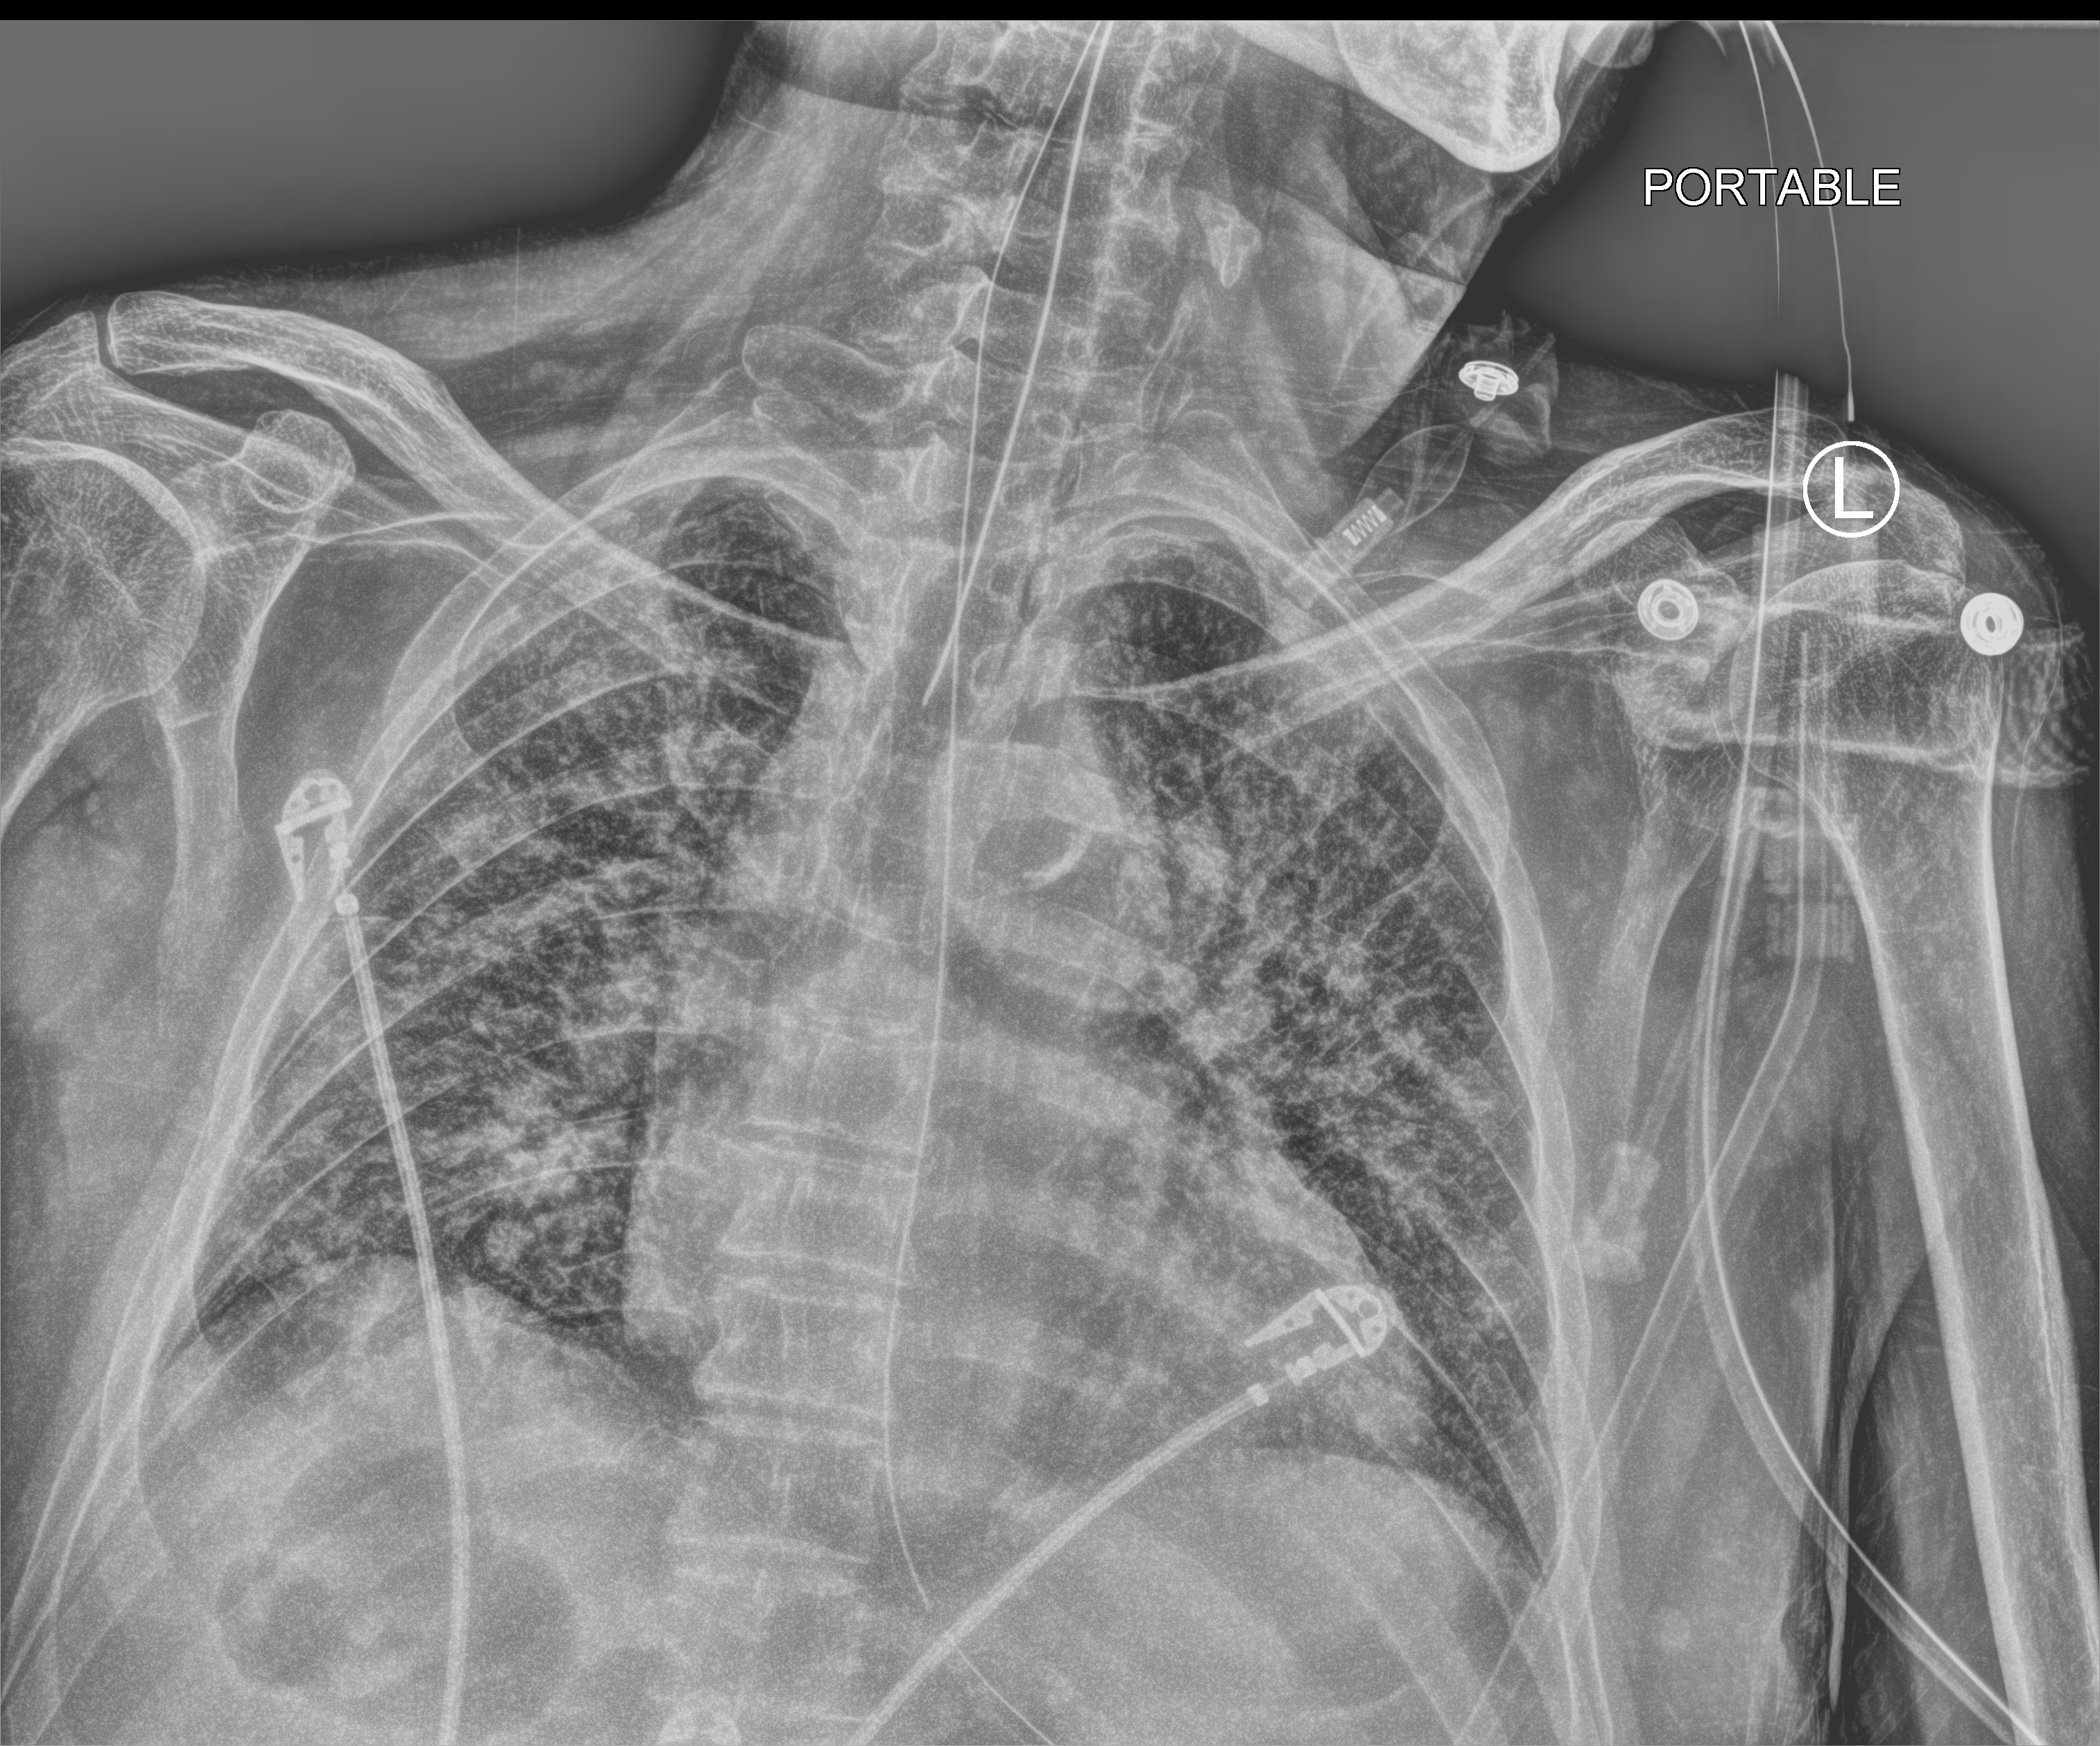
Chest X-ray (portable); anteroposterior (AP) projection. Male patient hospitalised with COVID-19, age 60–74 years.
Admission-level facts for this patient (not findings on this image; timing relative to this image not recorded):
- mechanically ventilated during this hospital stay: yes